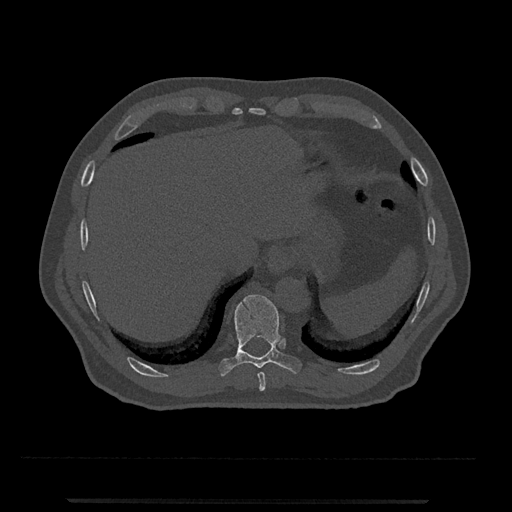
CT including the spine, one axial slice. Position 525 of 797 along the scan axis. Reconstruction kernel Br40s/3. Bone window (W 1800 / L 400 HU). 512 × 512 image matrix. Male patient, age 63 years. From the clinical record (not read from this slice): primary cancer: prostate.
Annotated regions visible in this slice (semi-automatic segmentation, software-assisted and operator-edited):
- T10 vertebra: bounding box <218,295,302,377> (left, top, right, bottom; pixels)
- T9 vertebra: <257,372,266,392>